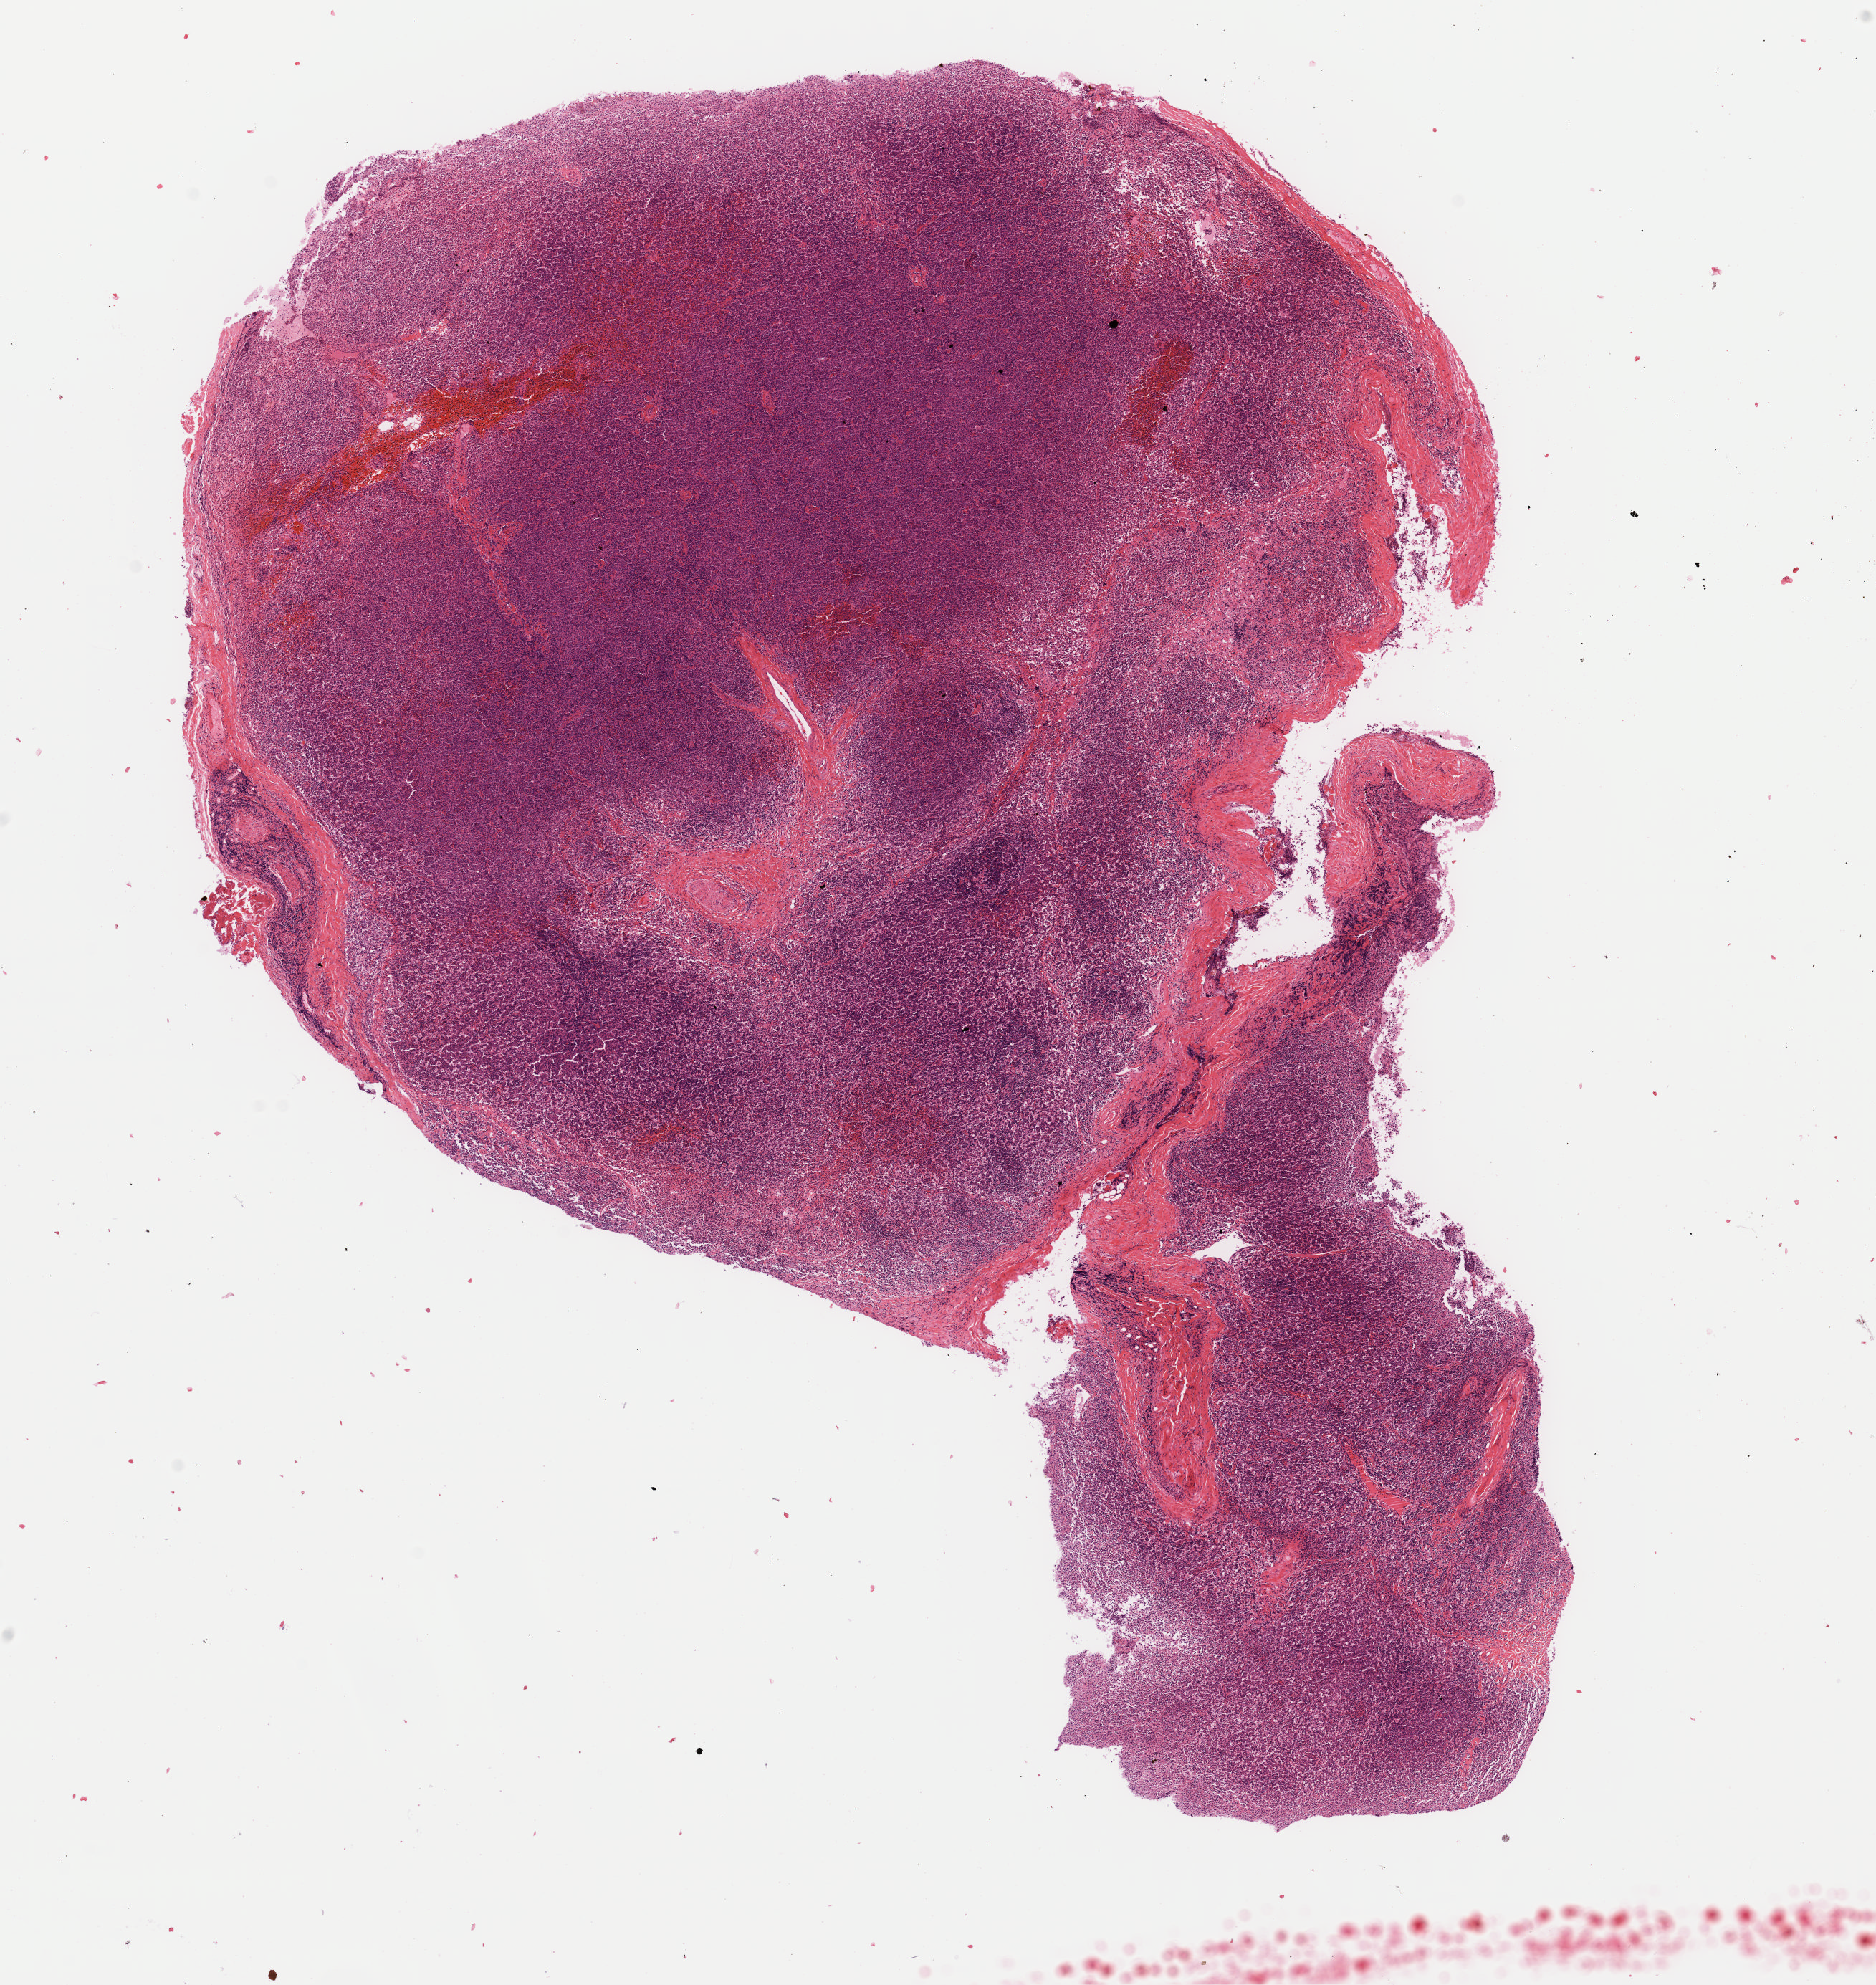
H&E-stained whole-slide image, whole scanned area (about 10.3 x 10.9 mm) shown as a low-resolution overview, formalin-fixed paraffin-embedded (FFPE) diagnostic section, primary tumour sample from the lymphoid tissue. Patient: male, age at initial diagnosis 73 years.
• pathologic diagnosis: Diffuse large B-cell lymphoma, NOS (lymph nodes of head, face and neck)